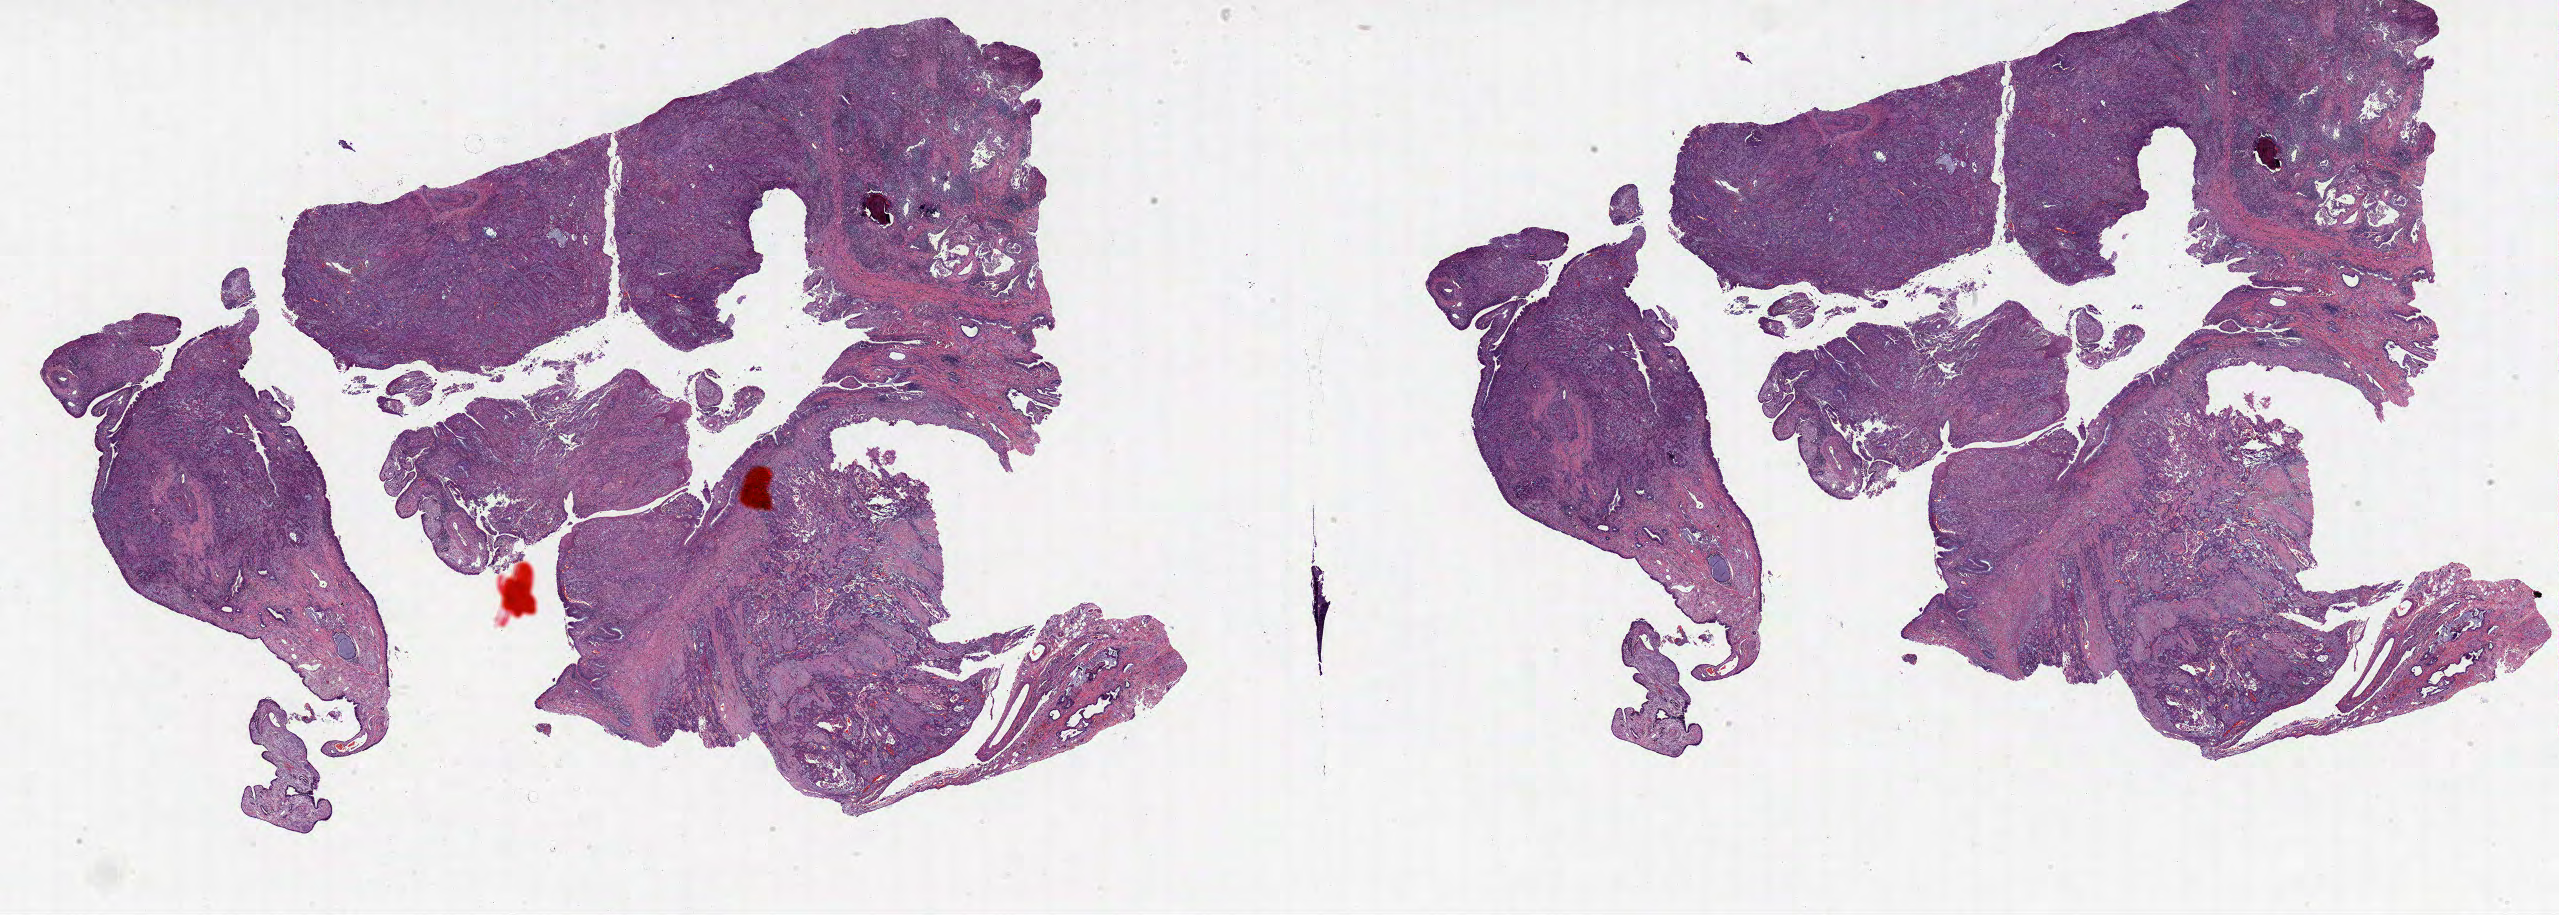
Whole-slide histology image, Hematoxylin and eosin (H&E) stained, shown as a low-resolution overview of the whole scanned area (about 41.3 x 14.8 mm, acquisition: 20x scan); FFPE section; sample: primary tumour, lung. Male, age 75 years at initial diagnosis.
Histologic diagnosis: Squamous cell carcinoma, NOS. AJCC pathologic stage: IIIA.